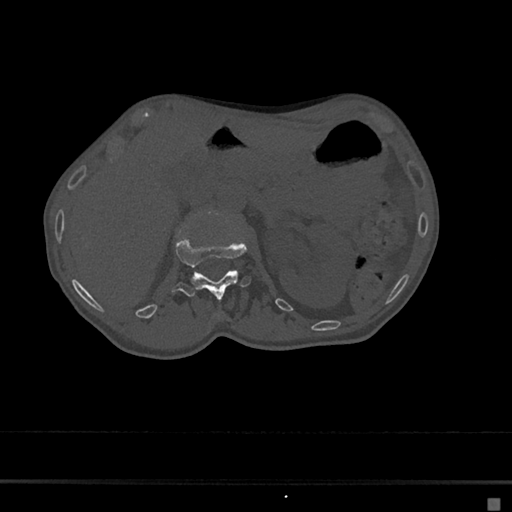
CT including the spine, one axial slice. Position 66 of 797 along the scan axis. Reconstruction kernel Br40s/3. 120 kVp. Bone window (W 1800 / L 400 HU). 0.5 mm slice thickness. 512 × 512 image matrix. Female patient, age 68 years. Case-level facts recorded for this patient, not image findings: primary cancer: renal.
Outlined on this slice (semi-automatically segmented with operator editing):
- L1 vertebra: bounding box <171,233,262,299> (left, top, right, bottom; pixels)